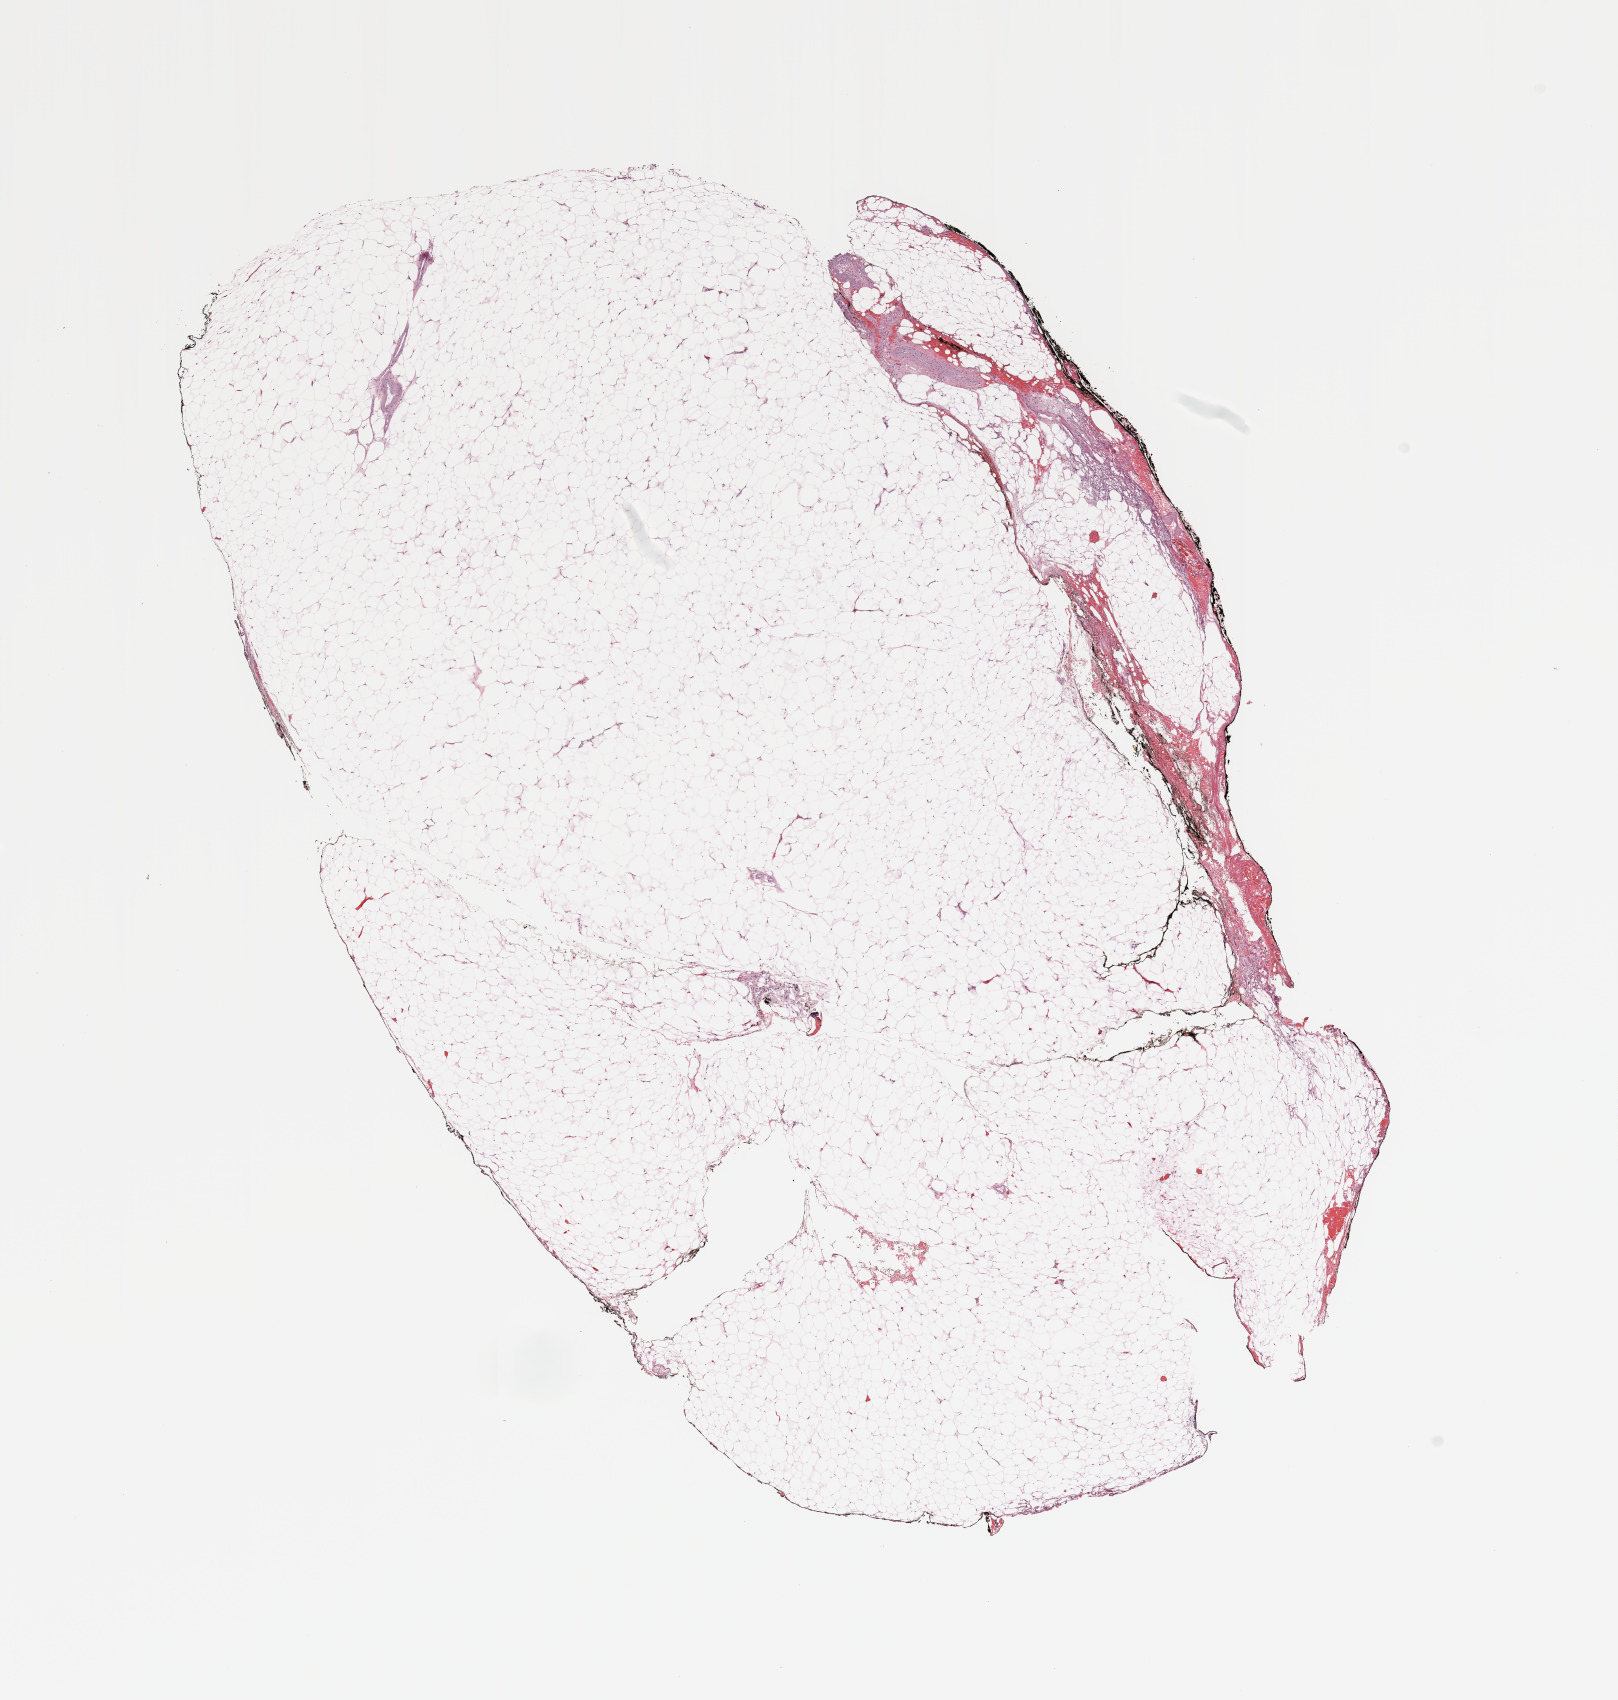
H&E whole-slide image, low-resolution overview of the scanned area, about 12.8 x 13.4 mm, kidney, normal (non-tumour) tissue. 54-year-old female patient.
This section: normal (non-tumour) tissue from the same patient. Patient diagnosis: Renal cell carcinoma, NOS.